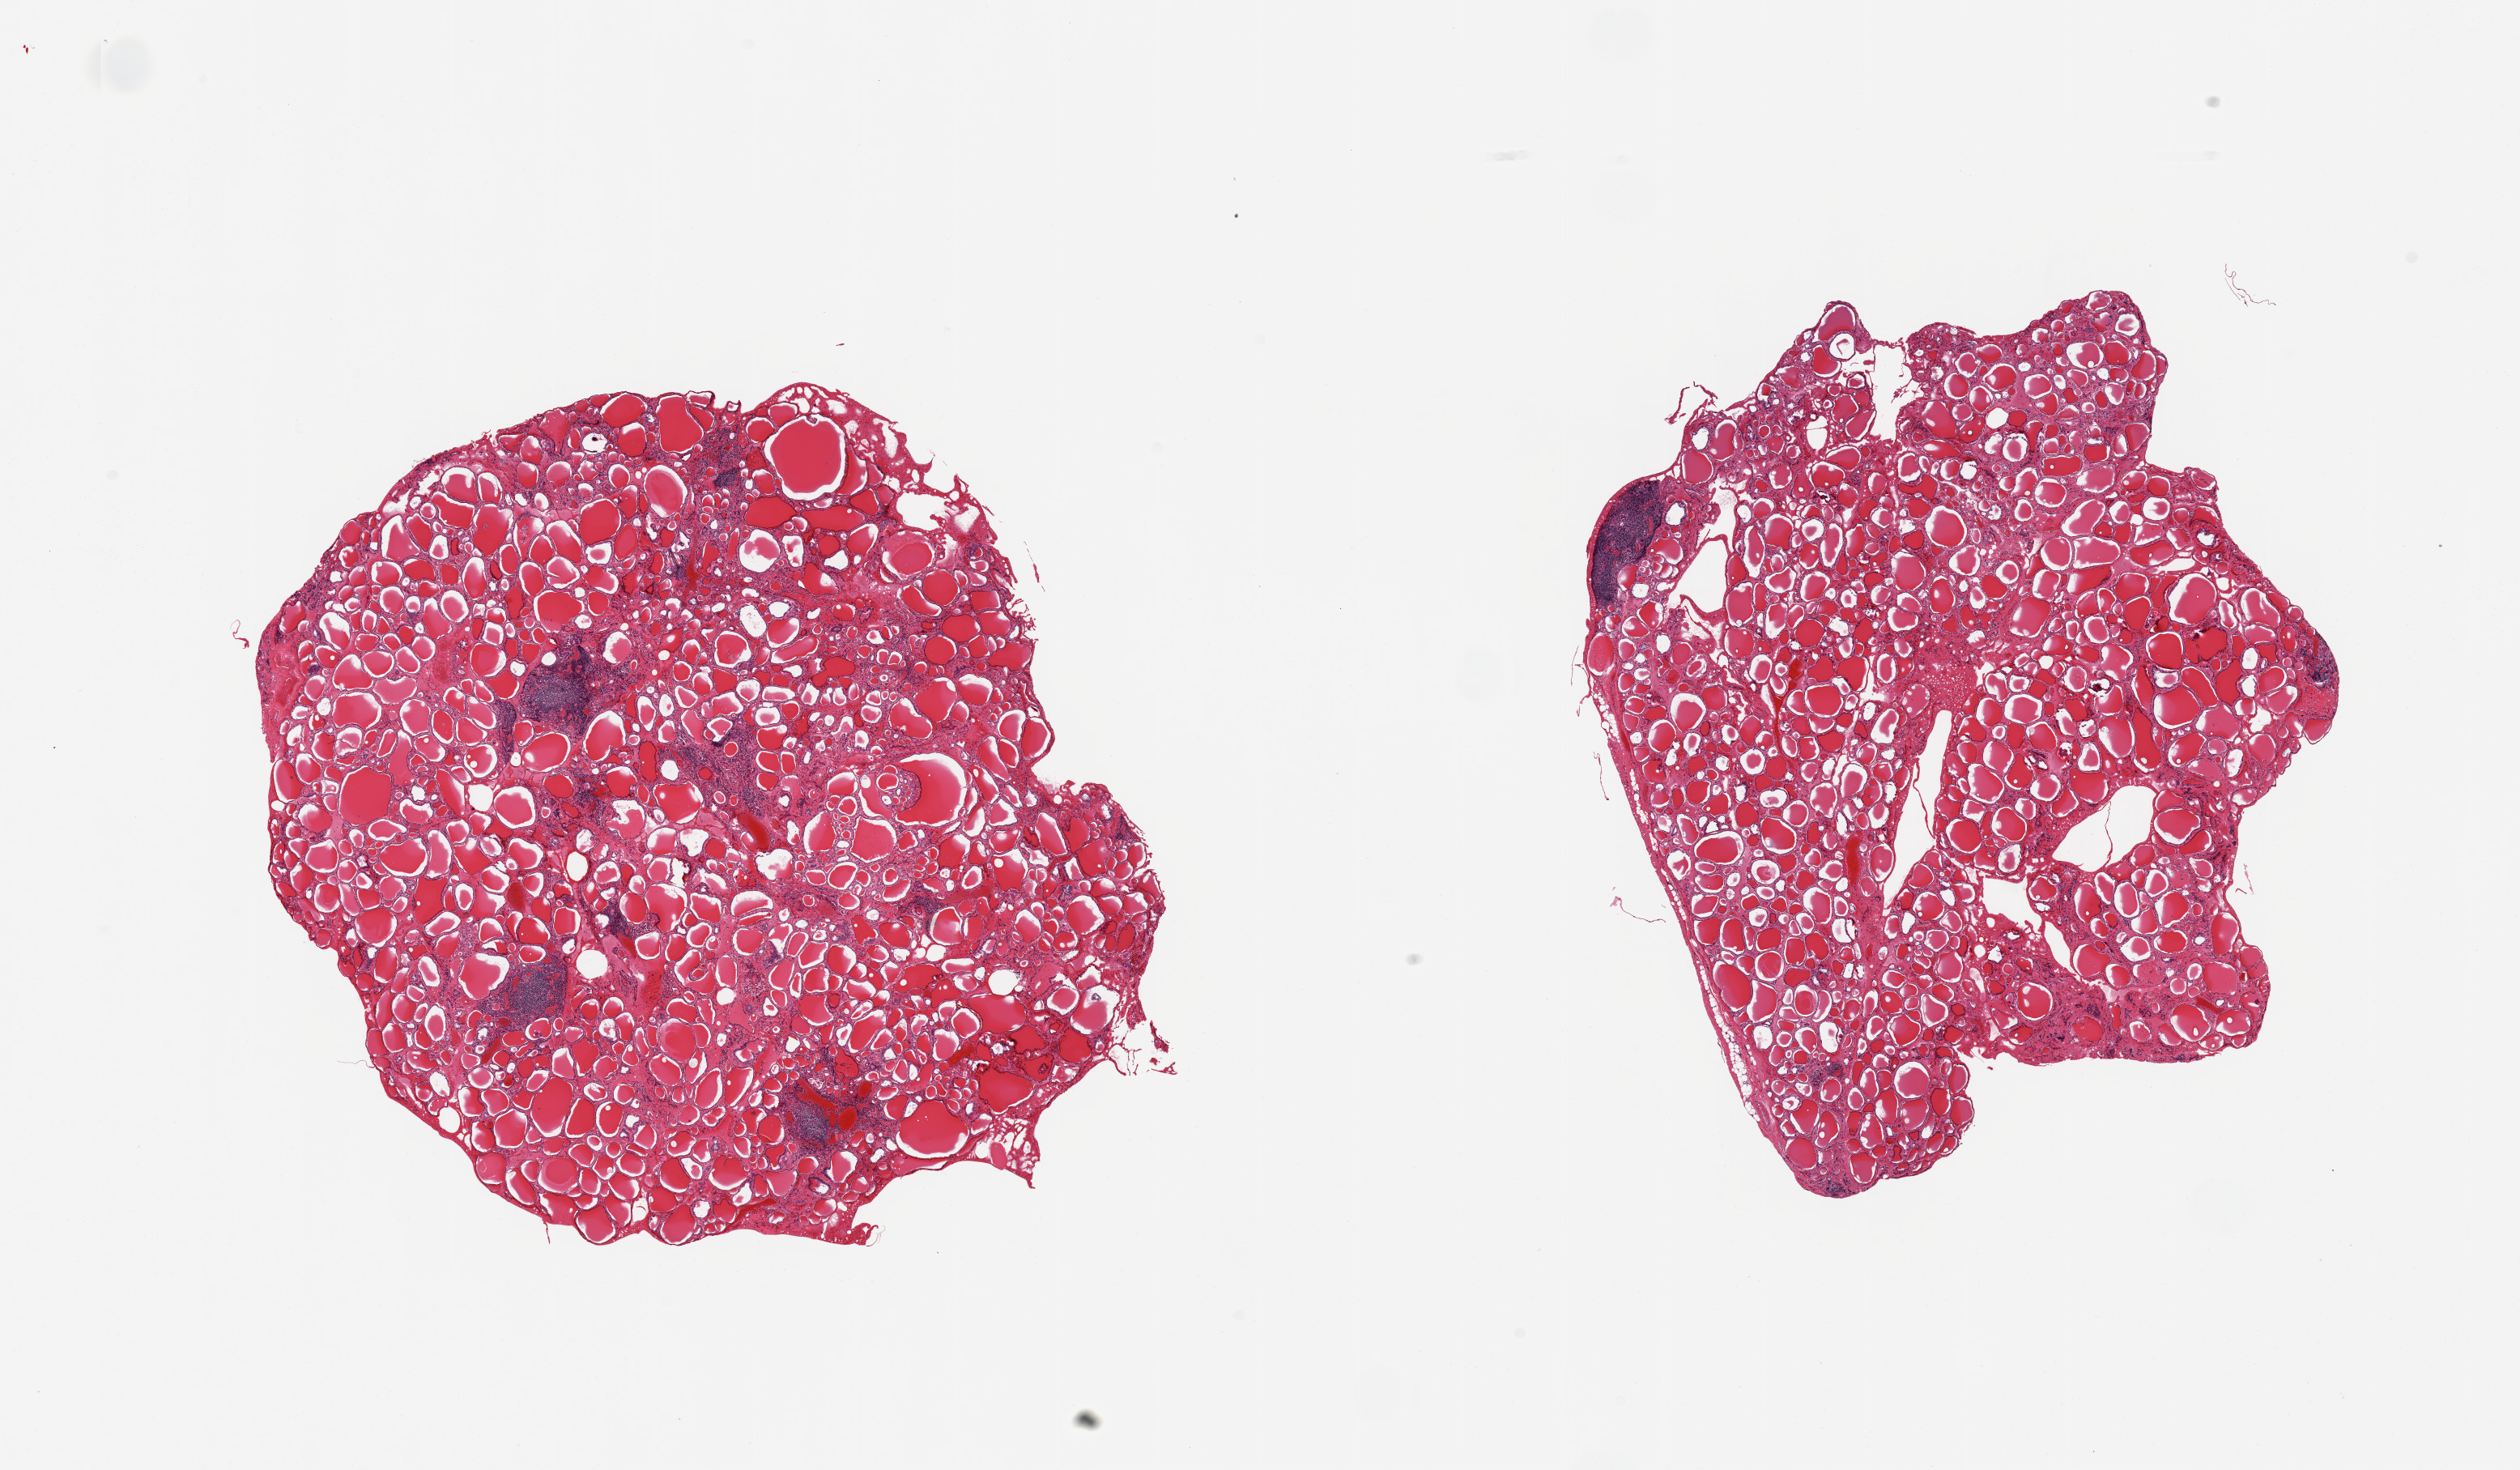
Digitized haematoxylin and eosin-stained section — whole scanned area (about 24.6 x 14.4 mm) shown as a low-resolution overview; PAXgene-fixed paraffin-embedded (PFPE) section; target tissue: thyroid; tissue donor sample. Male donor.
* pathologist's review note for this sample: 2 pieces, lymphocytic/Hashimoto thyroiditis, rep lymphoid aggregates